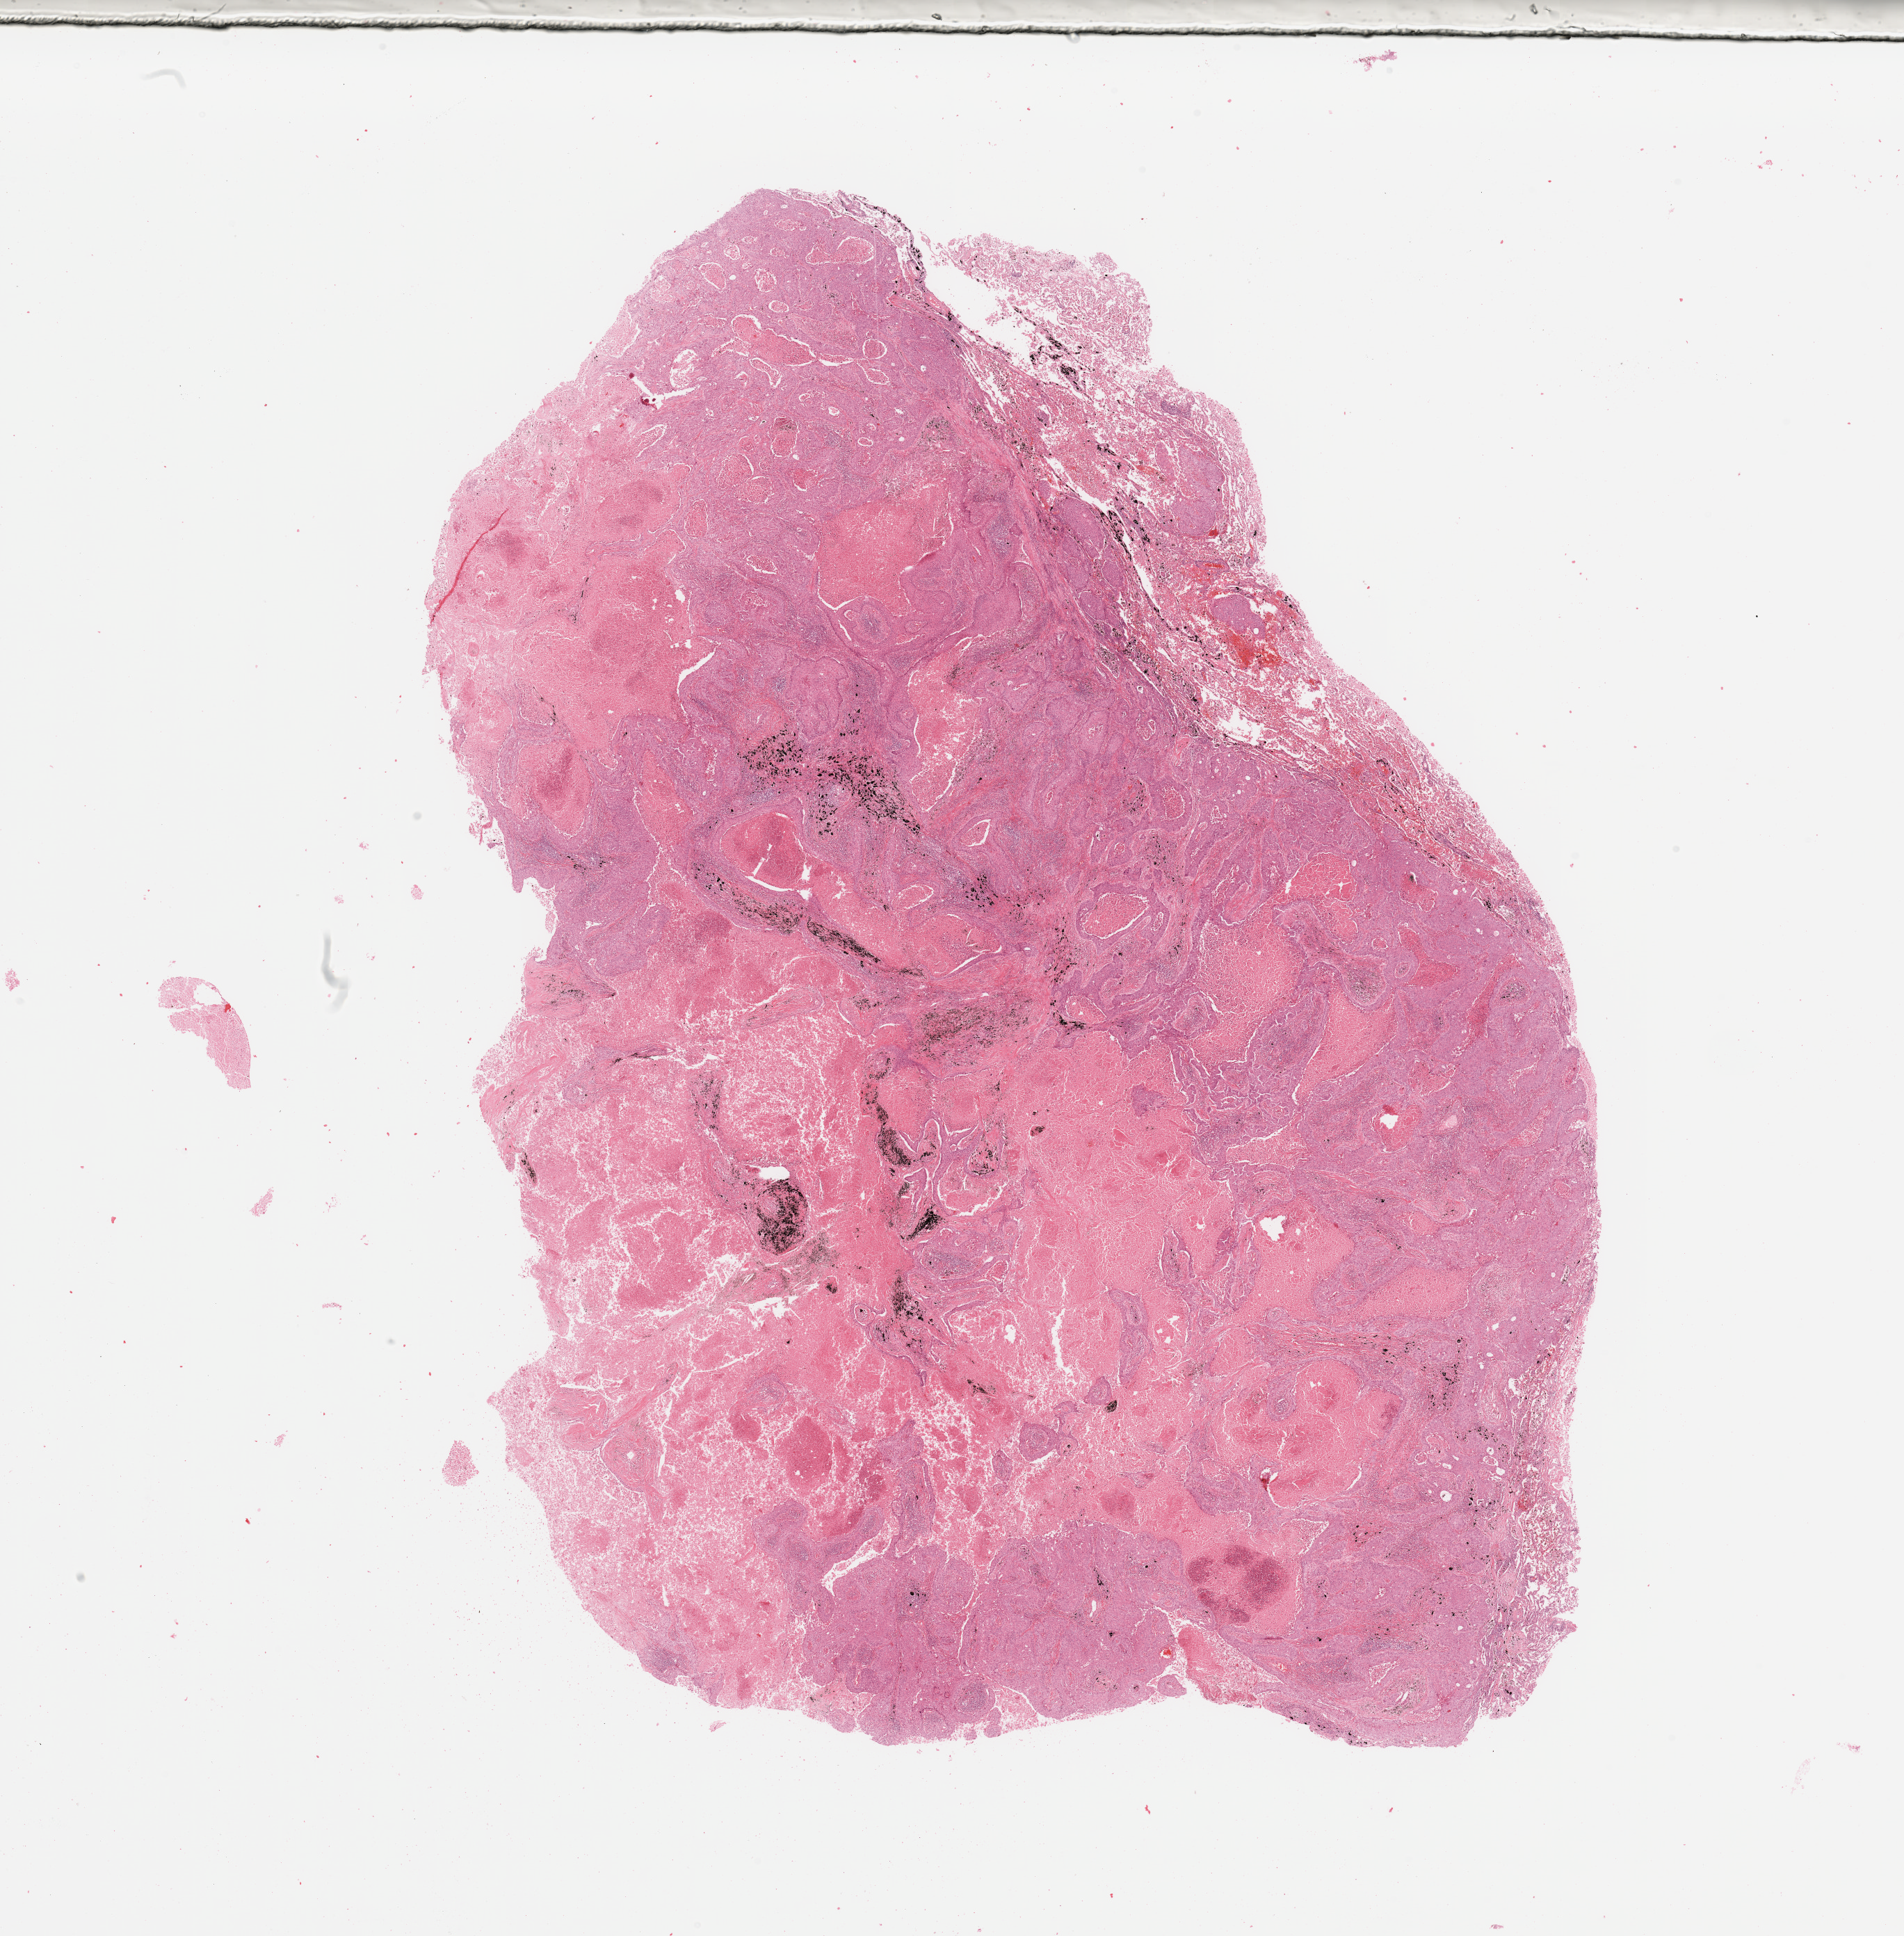
Digitized H&E tissue section (whole slide), low-resolution overview of the scanned area, about 21.7 x 22.0 mm (slide scanned at 20x). Lung, tumour tissue. Male, 56 y/o.
Histologic diagnosis: Squamous cell carcinoma, NOS.